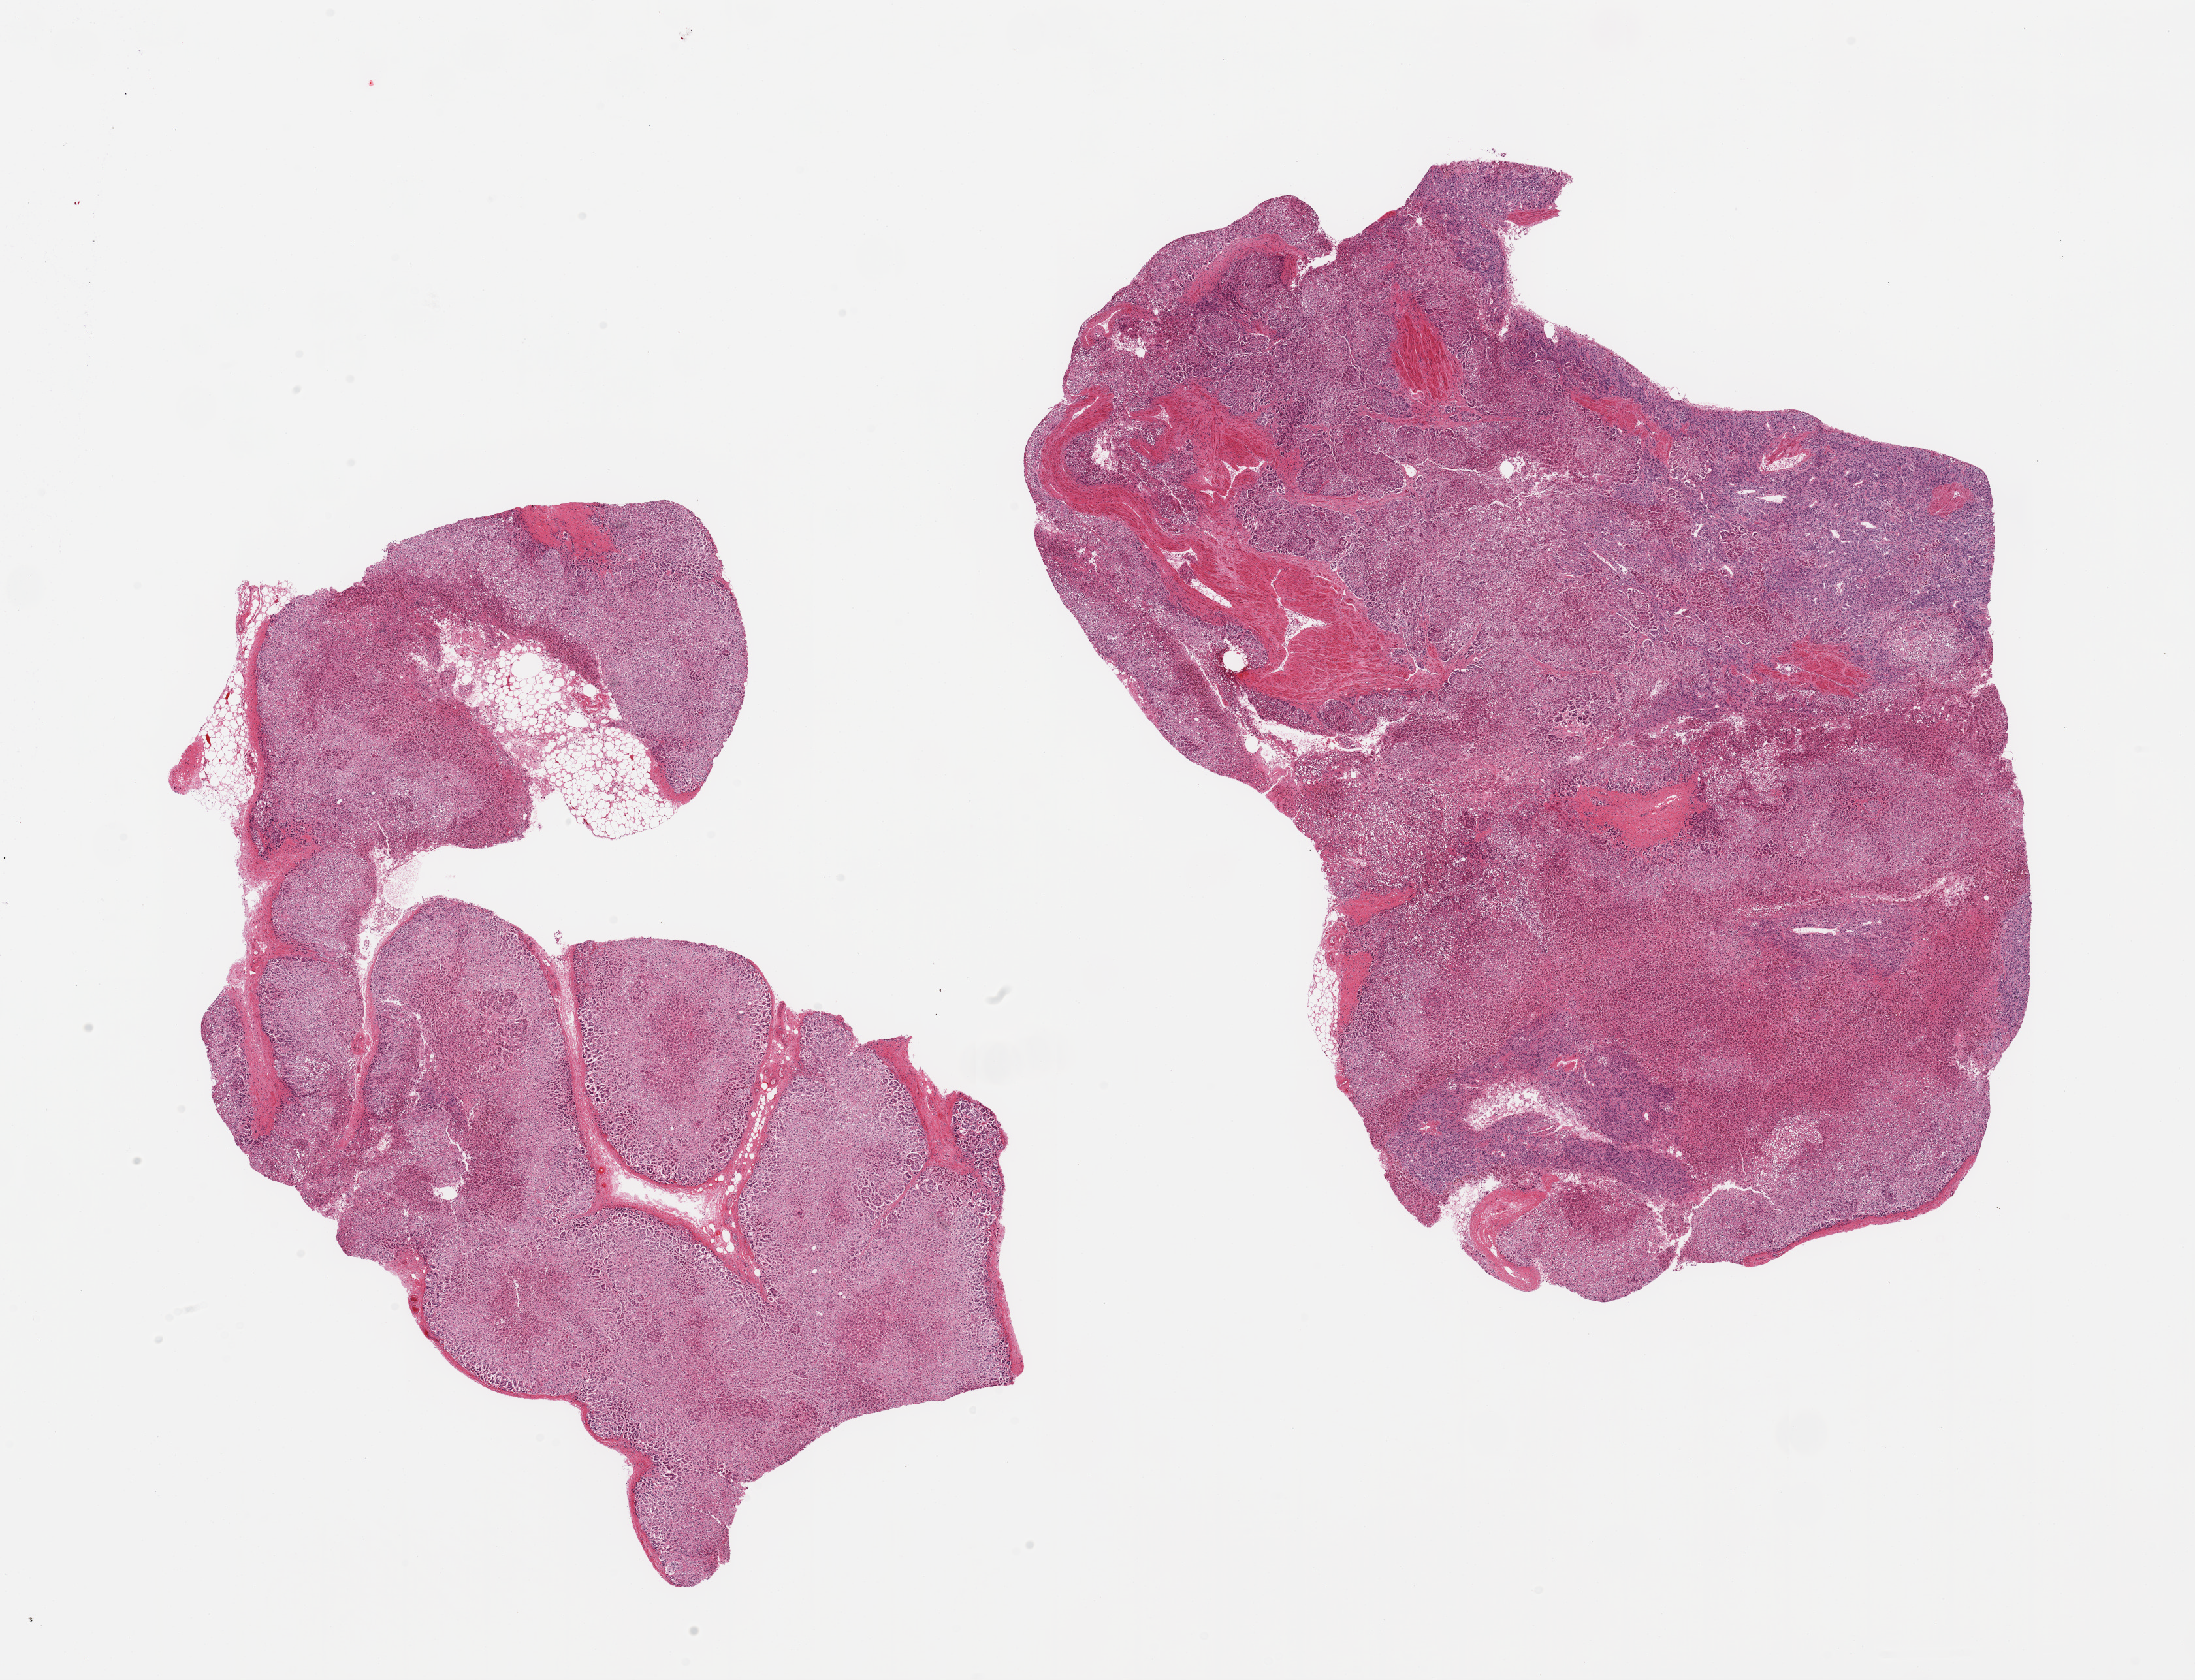
Haematoxylin and eosin whole-slide image, low-resolution overview of the scanned area, about 26.6 x 20.3 mm; PAXgene-fixed paraffin-embedded (PFPE) section; section of adrenal gland (target tissue); tissue donor sample. Donor sex: male.
Pathologist's review note for this sample: 2 pieces; larger piece has areas of moderate autolysis; 10% fat in smaller piece.